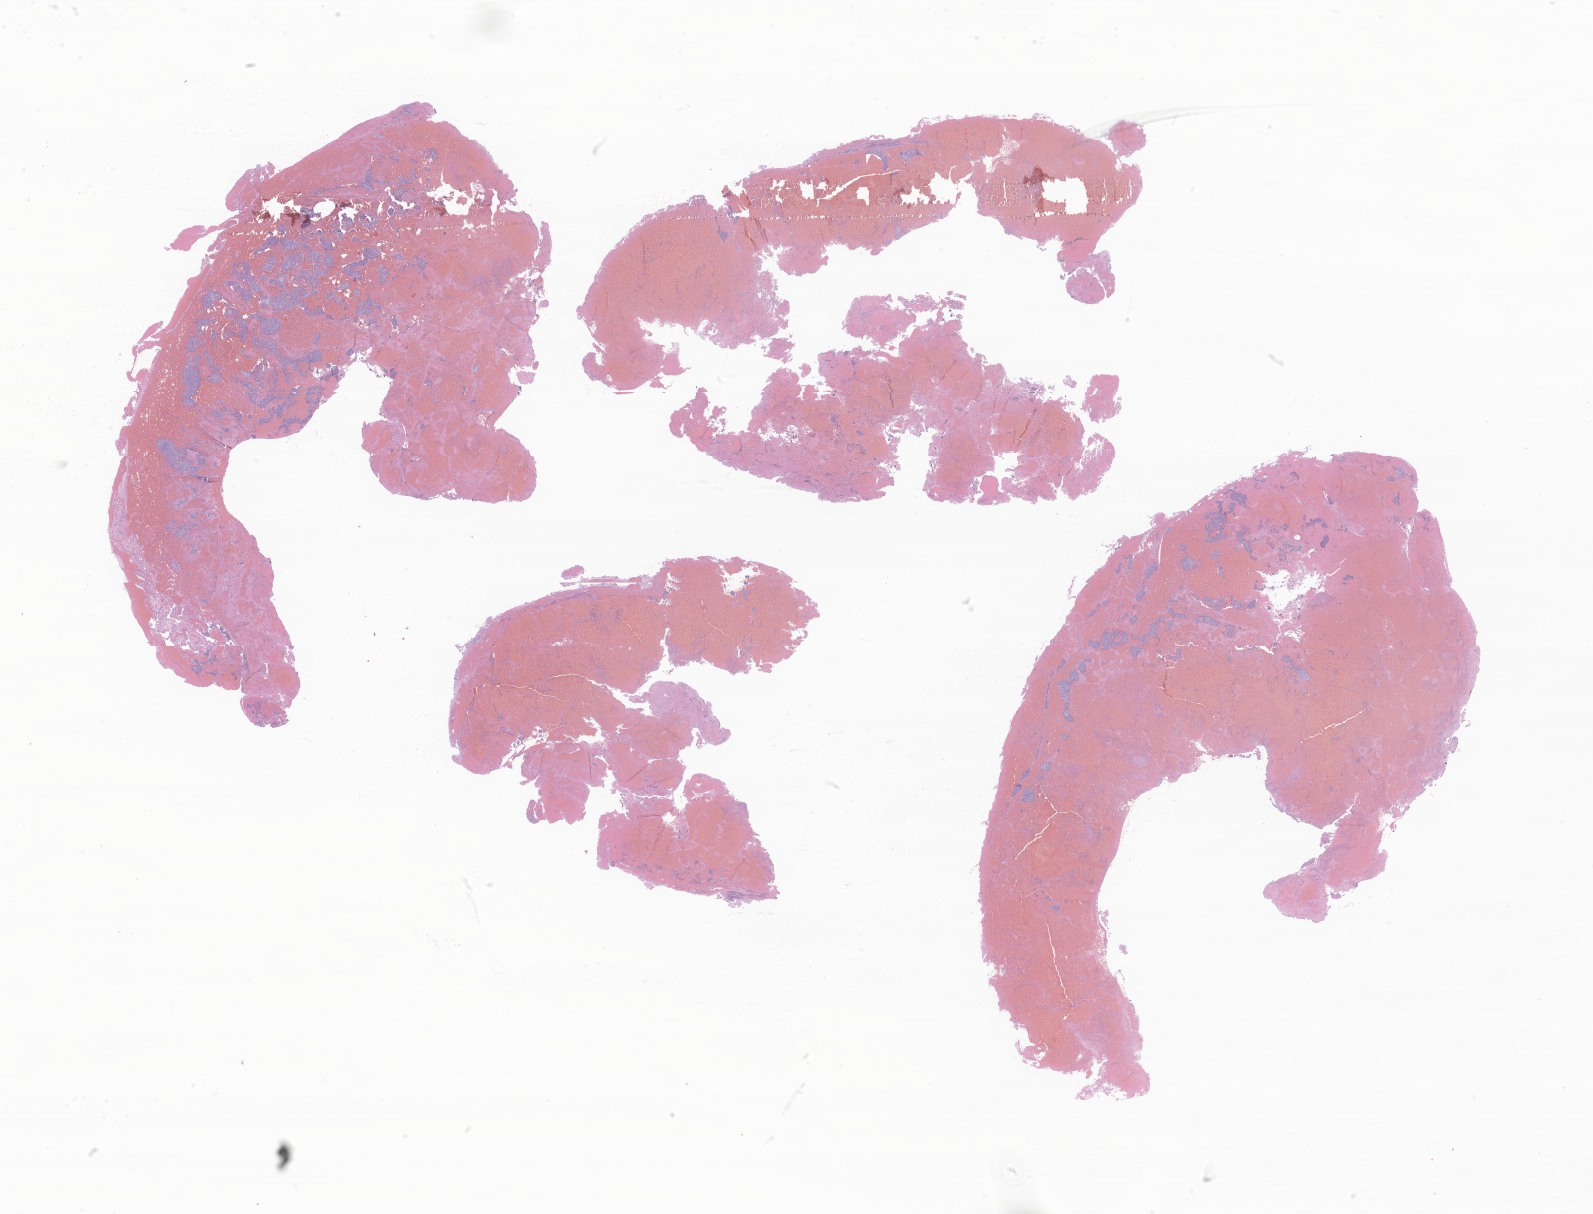
Whole-slide image, haematoxylin and eosin stain of tumor tissue from the brain — whole scanned area (about 26.9 x 20.5 mm) shown as a low-resolution overview, formalin-fixed paraffin-embedded section. Patient female; age 140 months (11 years 8 months).
Recorded diagnosis: Medulloblastoma, NOS.